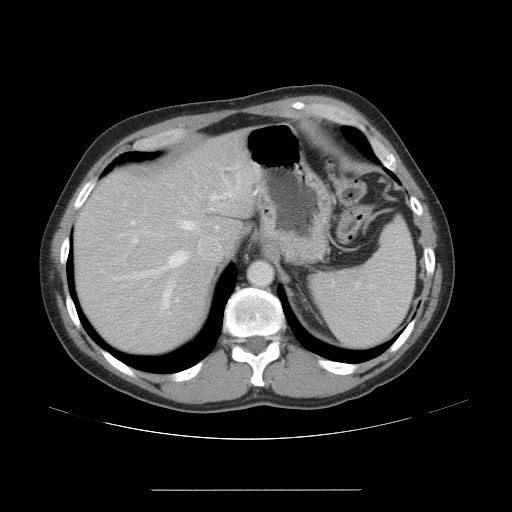
Contrast-enhanced abdominal CT, one axial slice; 120 kVp; intravenous contrast given; soft-tissue window (W 400 / L 40 HU); 5 mm slice thickness; 512 × 512 image matrix, field of view 409 × 409 mm. Male patient, age 56 years. Case-level facts recorded for this patient, not image findings: diagnosis: colorectal cancer liver metastases, imaged before liver resection; multiple liver metastases: yes; largest metastasis: 1.8 cm.
Outlined on this slice (manually delineated by an expert):
- hepatic veins: box from (x=113, y=194) to (x=231, y=310) px
- liver: (x=78, y=137)–(x=252, y=352)
- planned liver remnant (the part of the liver to remain after resection): (x=79, y=137)–(x=252, y=352)
- portal vein (with intrahepatic branches): (x=130, y=220)–(x=138, y=245)